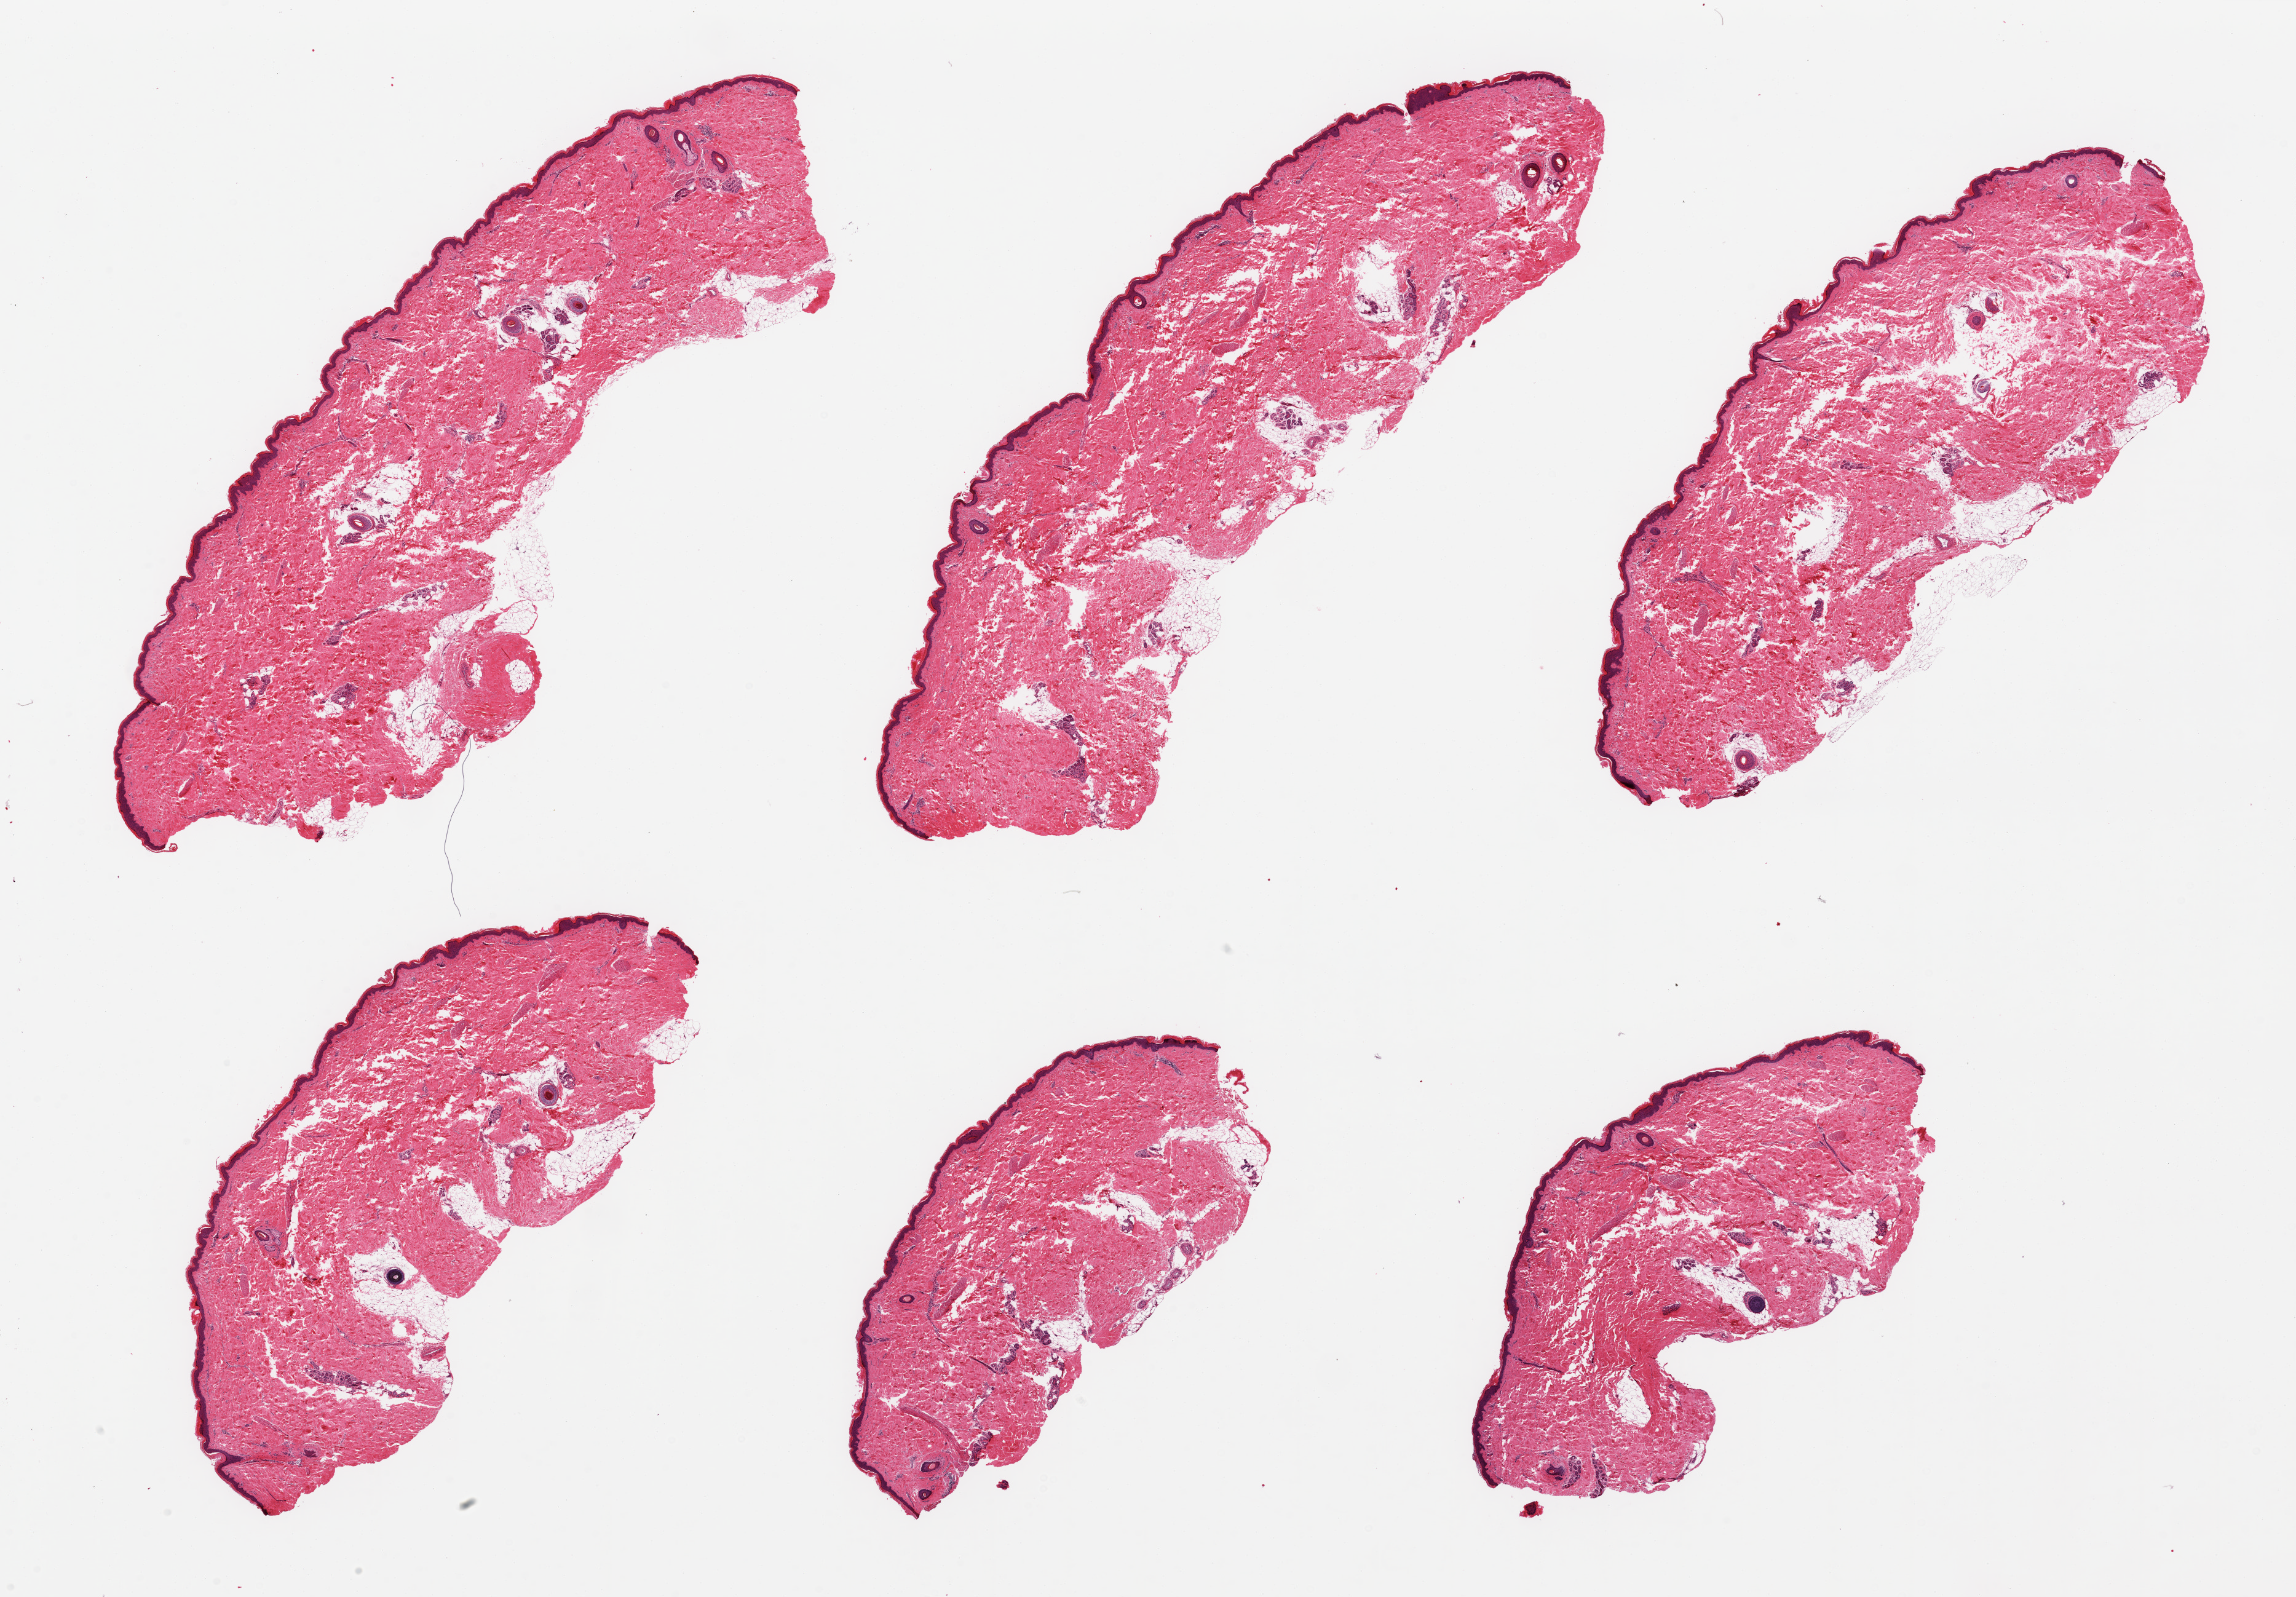
Digitized H&E-stained section — whole scanned area (about 29.5 x 20.5 mm) shown as a low-resolution overview, PAXgene-fixed, paraffin-embedded tissue, sampled site (target tissue): skin of lower leg, donor tissue sample. Donor: male.
Review note (as recorded): 6 pieces, moderate dermal fat; squamous epithelium is ~50-60 microns.